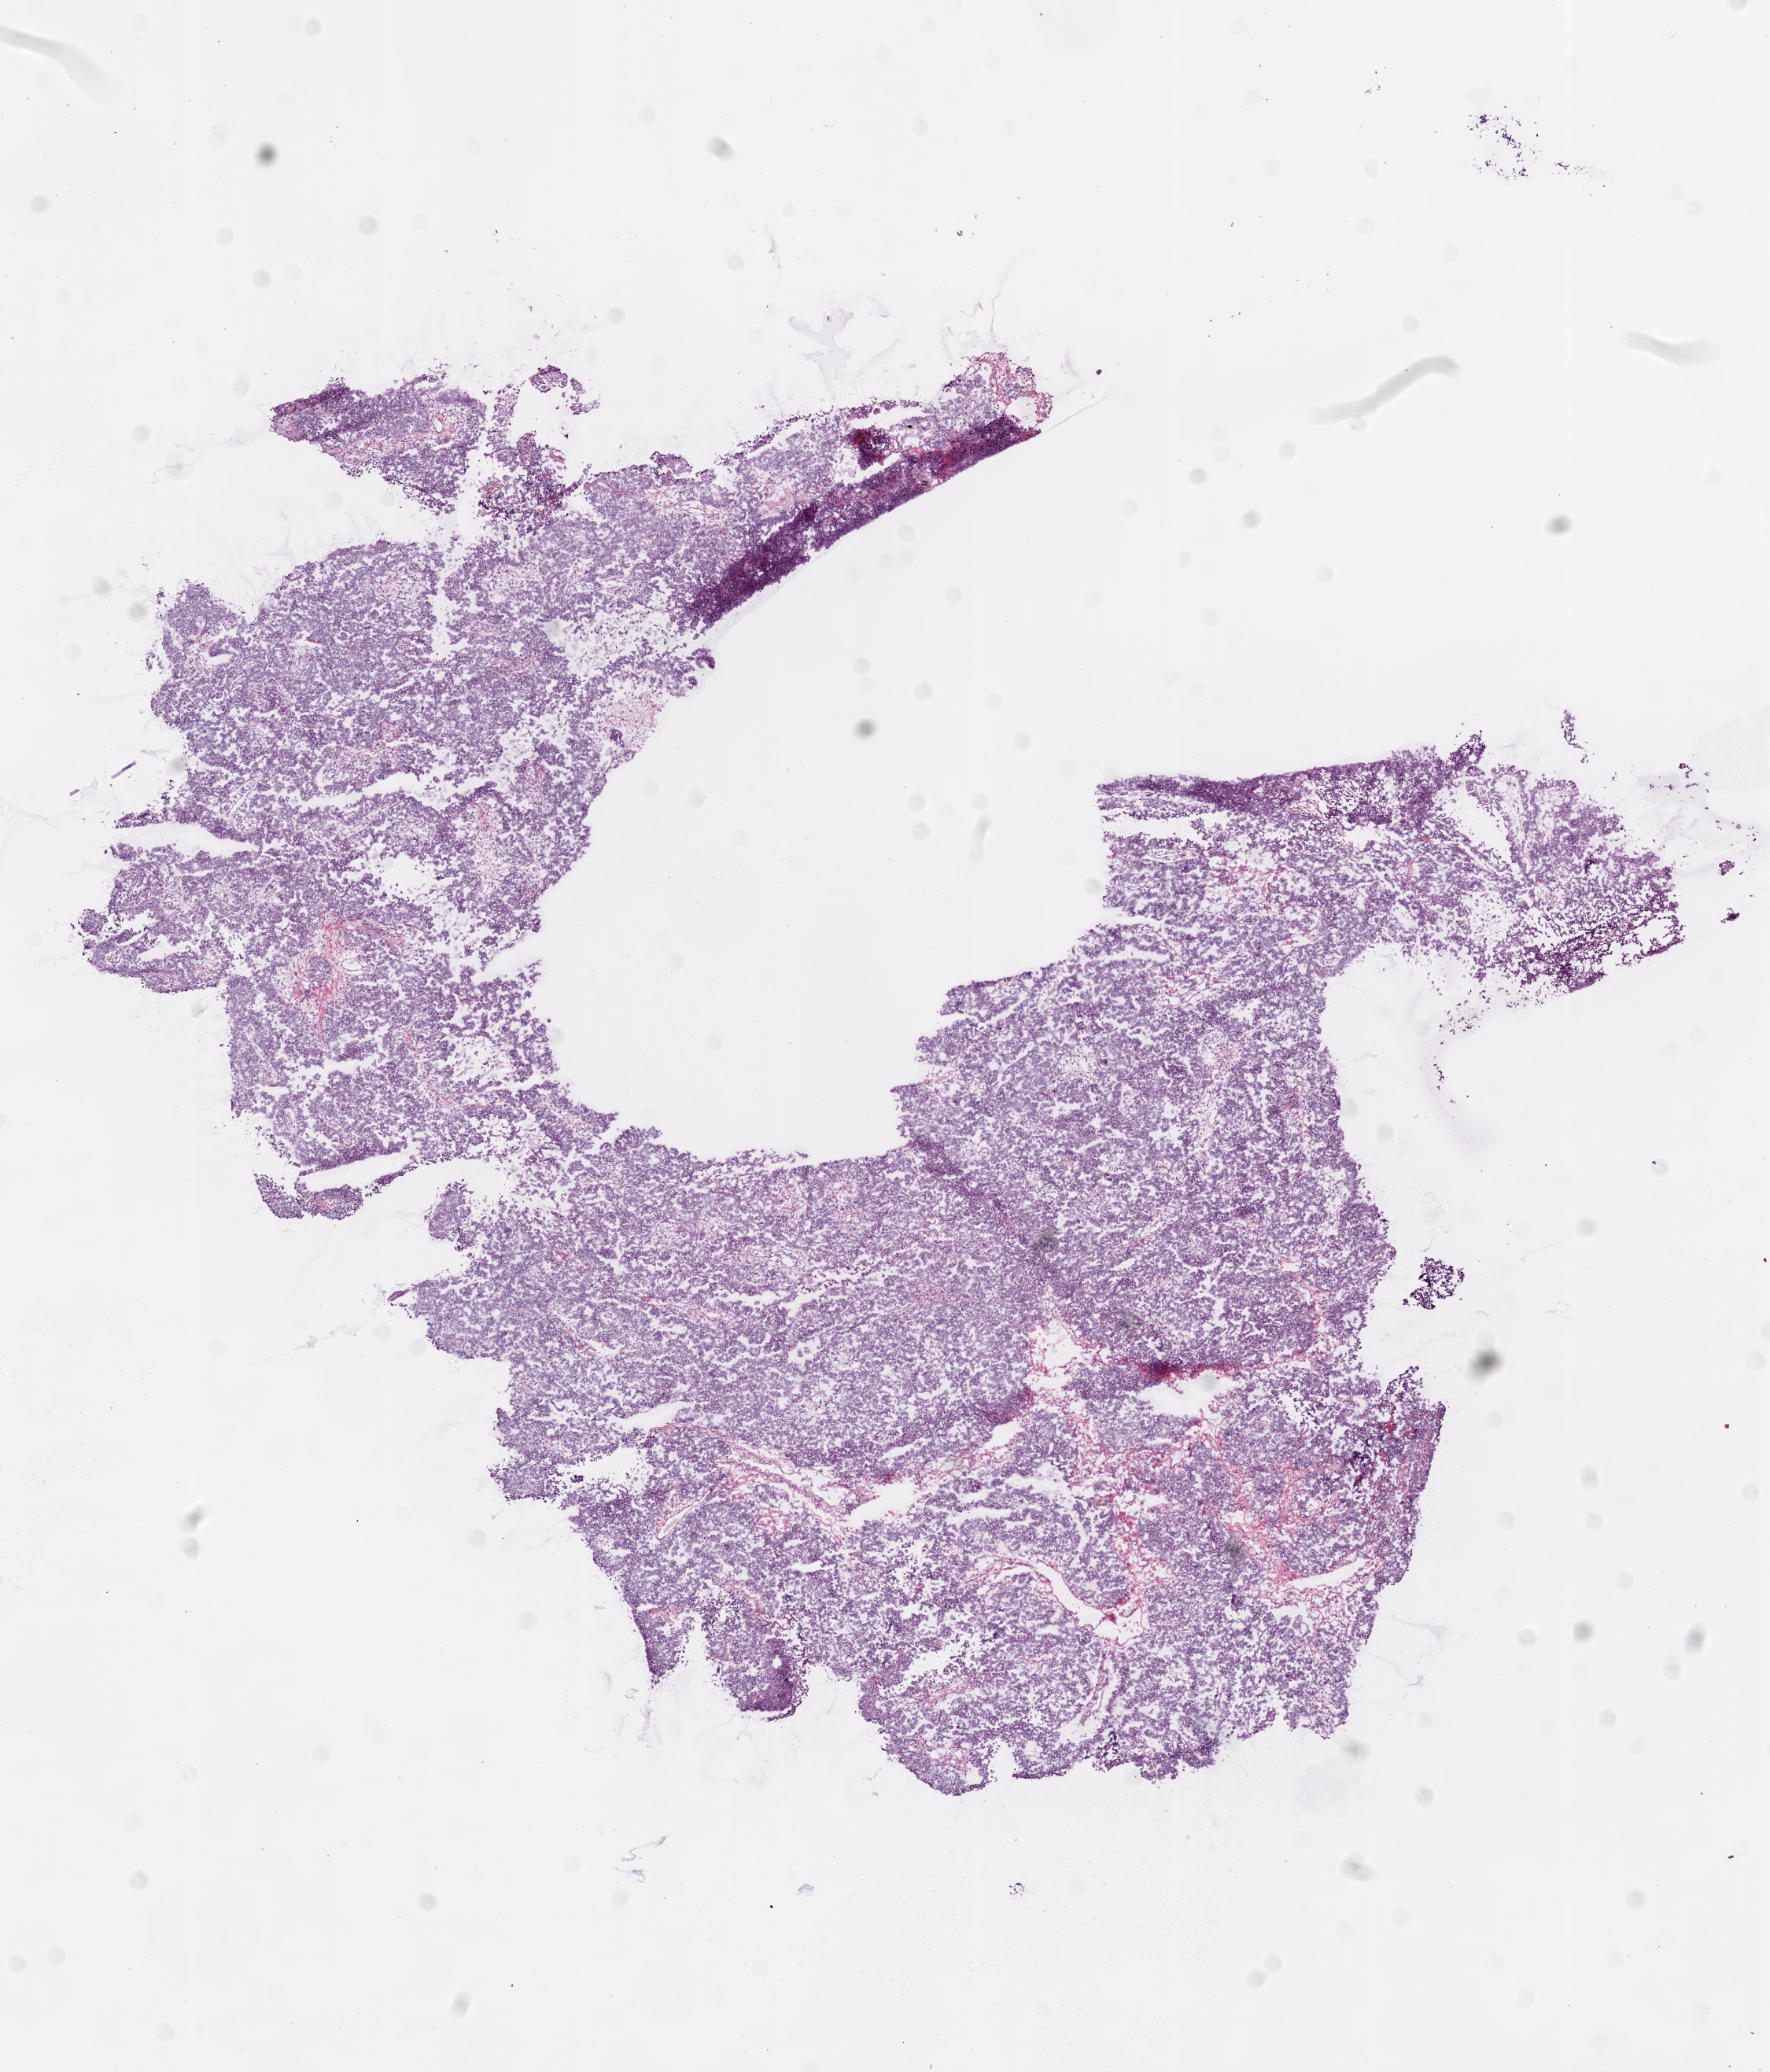
H&E-stained whole-slide image, low-resolution overview of the scanned area, about 9.0 x 10.6 mm. Frozen section from the bottom of the tissue portion. Primary tumour sample from the ovary. Female, age 63 years at initial diagnosis. Histologic grade: G3 (poorly differentiated). Slide review estimates, as recorded: tumour cells 94%, tumour nuclei 95%, normal cells 0%, stromal cells 5%, necrosis 1%.
Laterality: bilateral. Histologic diagnosis: Serous cystadenocarcinoma, NOS. FIGO stage: IIIC.